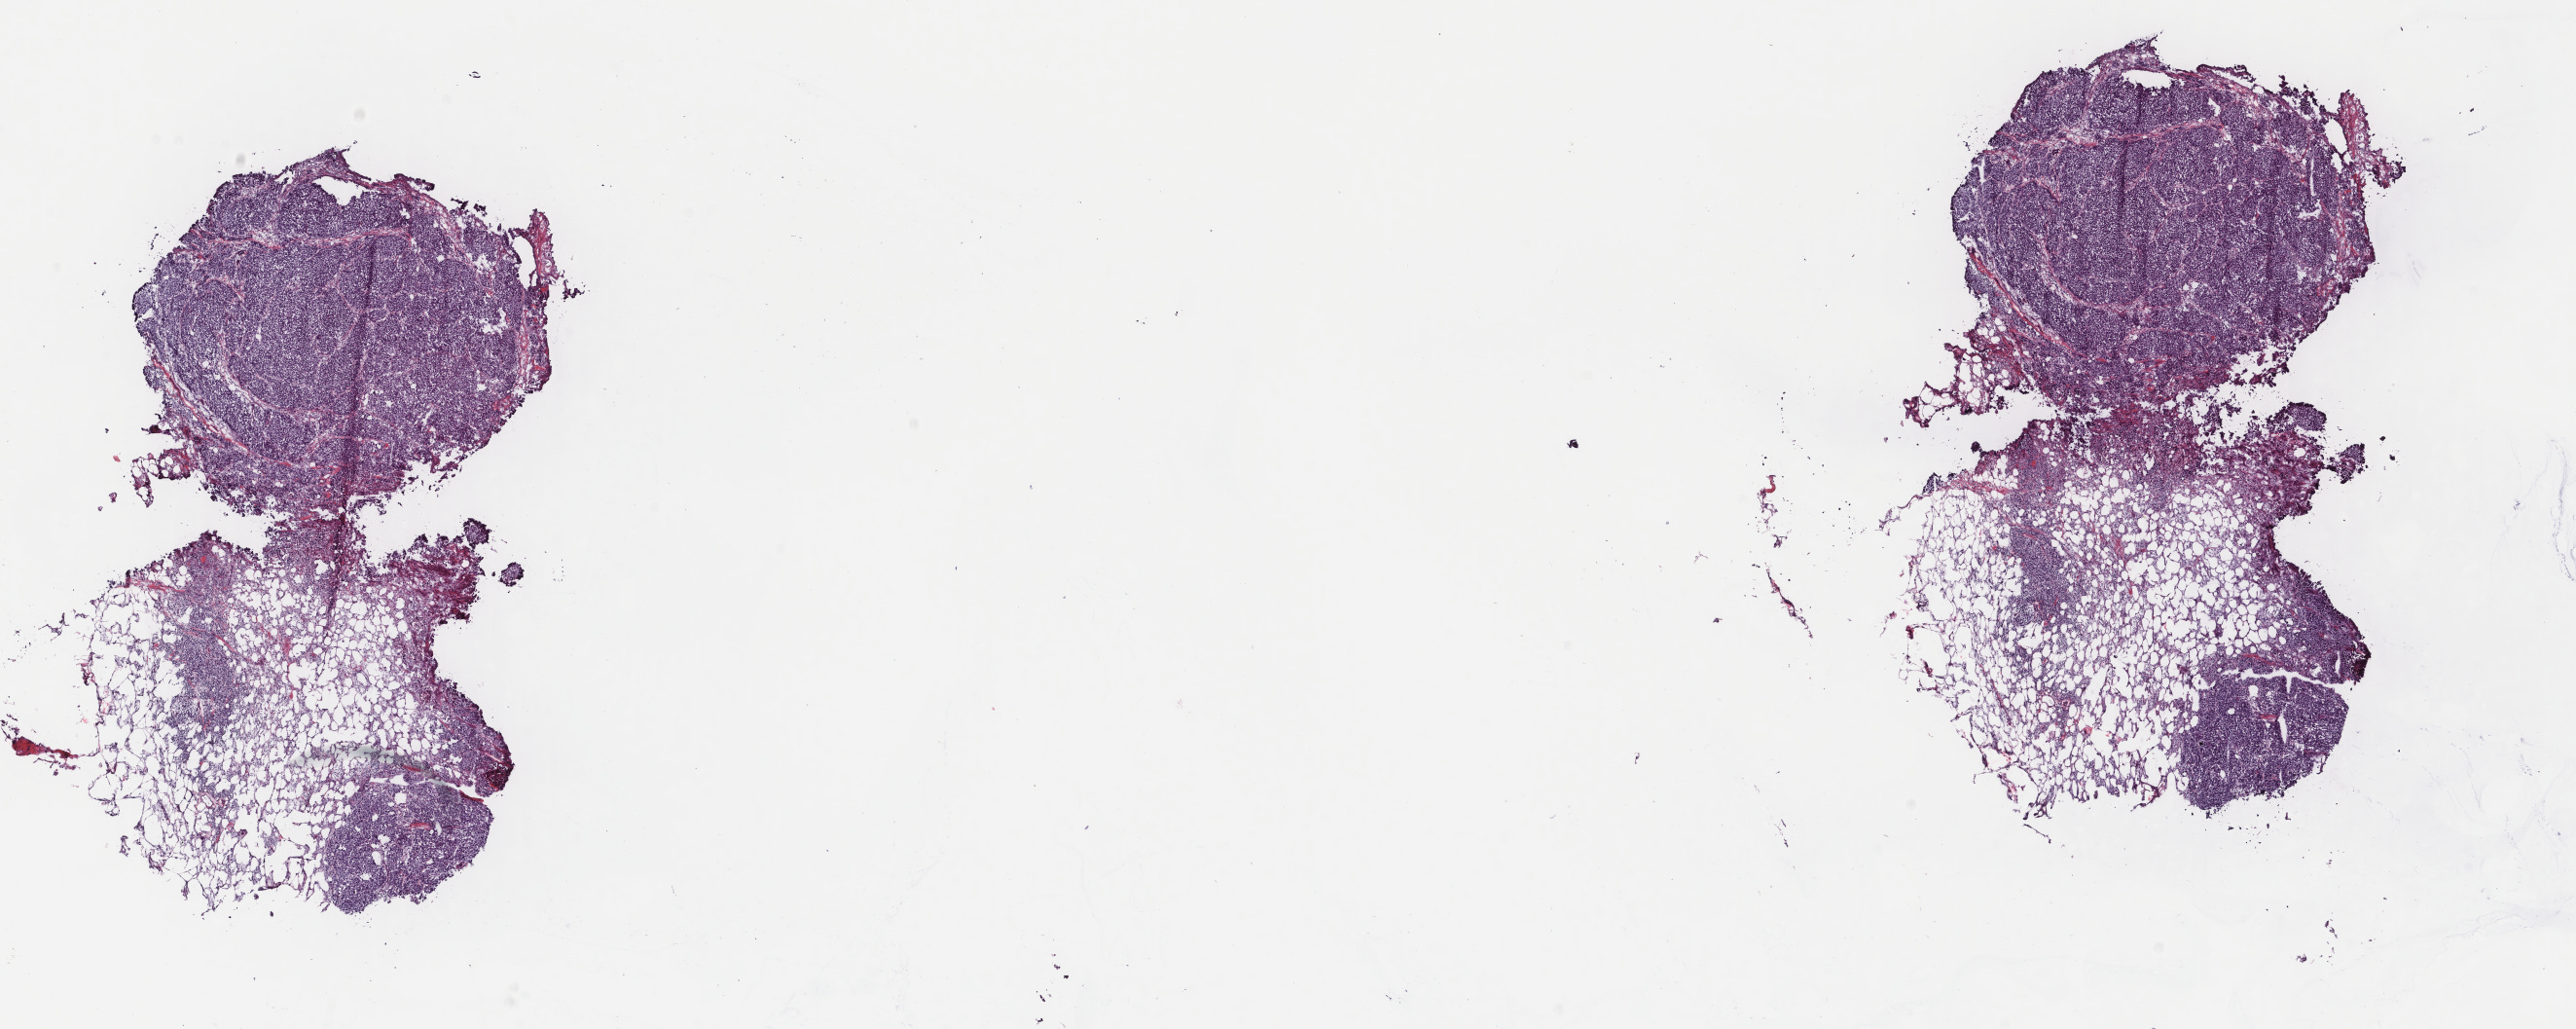
Hematoxylin and eosin (H&E) stained whole-slide image — a low-resolution overview of the entire scanned area, about 21.0 x 8.4 mm (from a 40x scan), frozen section, breast, primary tumour sample. Female patient; age at initial diagnosis 45 years. Composition of this section per pathologist review: tumour cells 65%, tumour nuclei 85%, normal cells 0%, stromal cells 35%, necrosis 0%. Inflammatory infiltration, as recorded: lymphocyte infiltration 0%, monocyte infiltration 0%, neutrophil infiltration 0%.
Lymph nodes positive (case pathology): 1 of 13 examined. AJCC pathologic stage: IIB (6th edition). Diagnosis: Infiltrating duct carcinoma, NOS. Laterality: left.